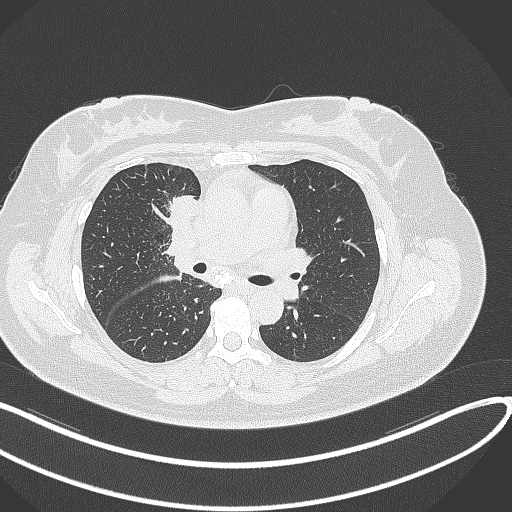
Chest CT, one axial slice; position 160 of 303 along the scan axis; 120 kVp; lung window (W 1500 / L -600 HU); 512 × 512 image matrix, field of view 400 × 400 mm. Female patient, age 46 years. From the clinical record (not read from this slice): clinical TNM (as recorded): T2a N1 M0.
Annotated regions visible in this slice (bounding box drawn by a radiologist):
- lung tumour (recorded histology: adenocarcinoma): bounding box <166,190,198,231> (left, top, right, bottom; pixels)